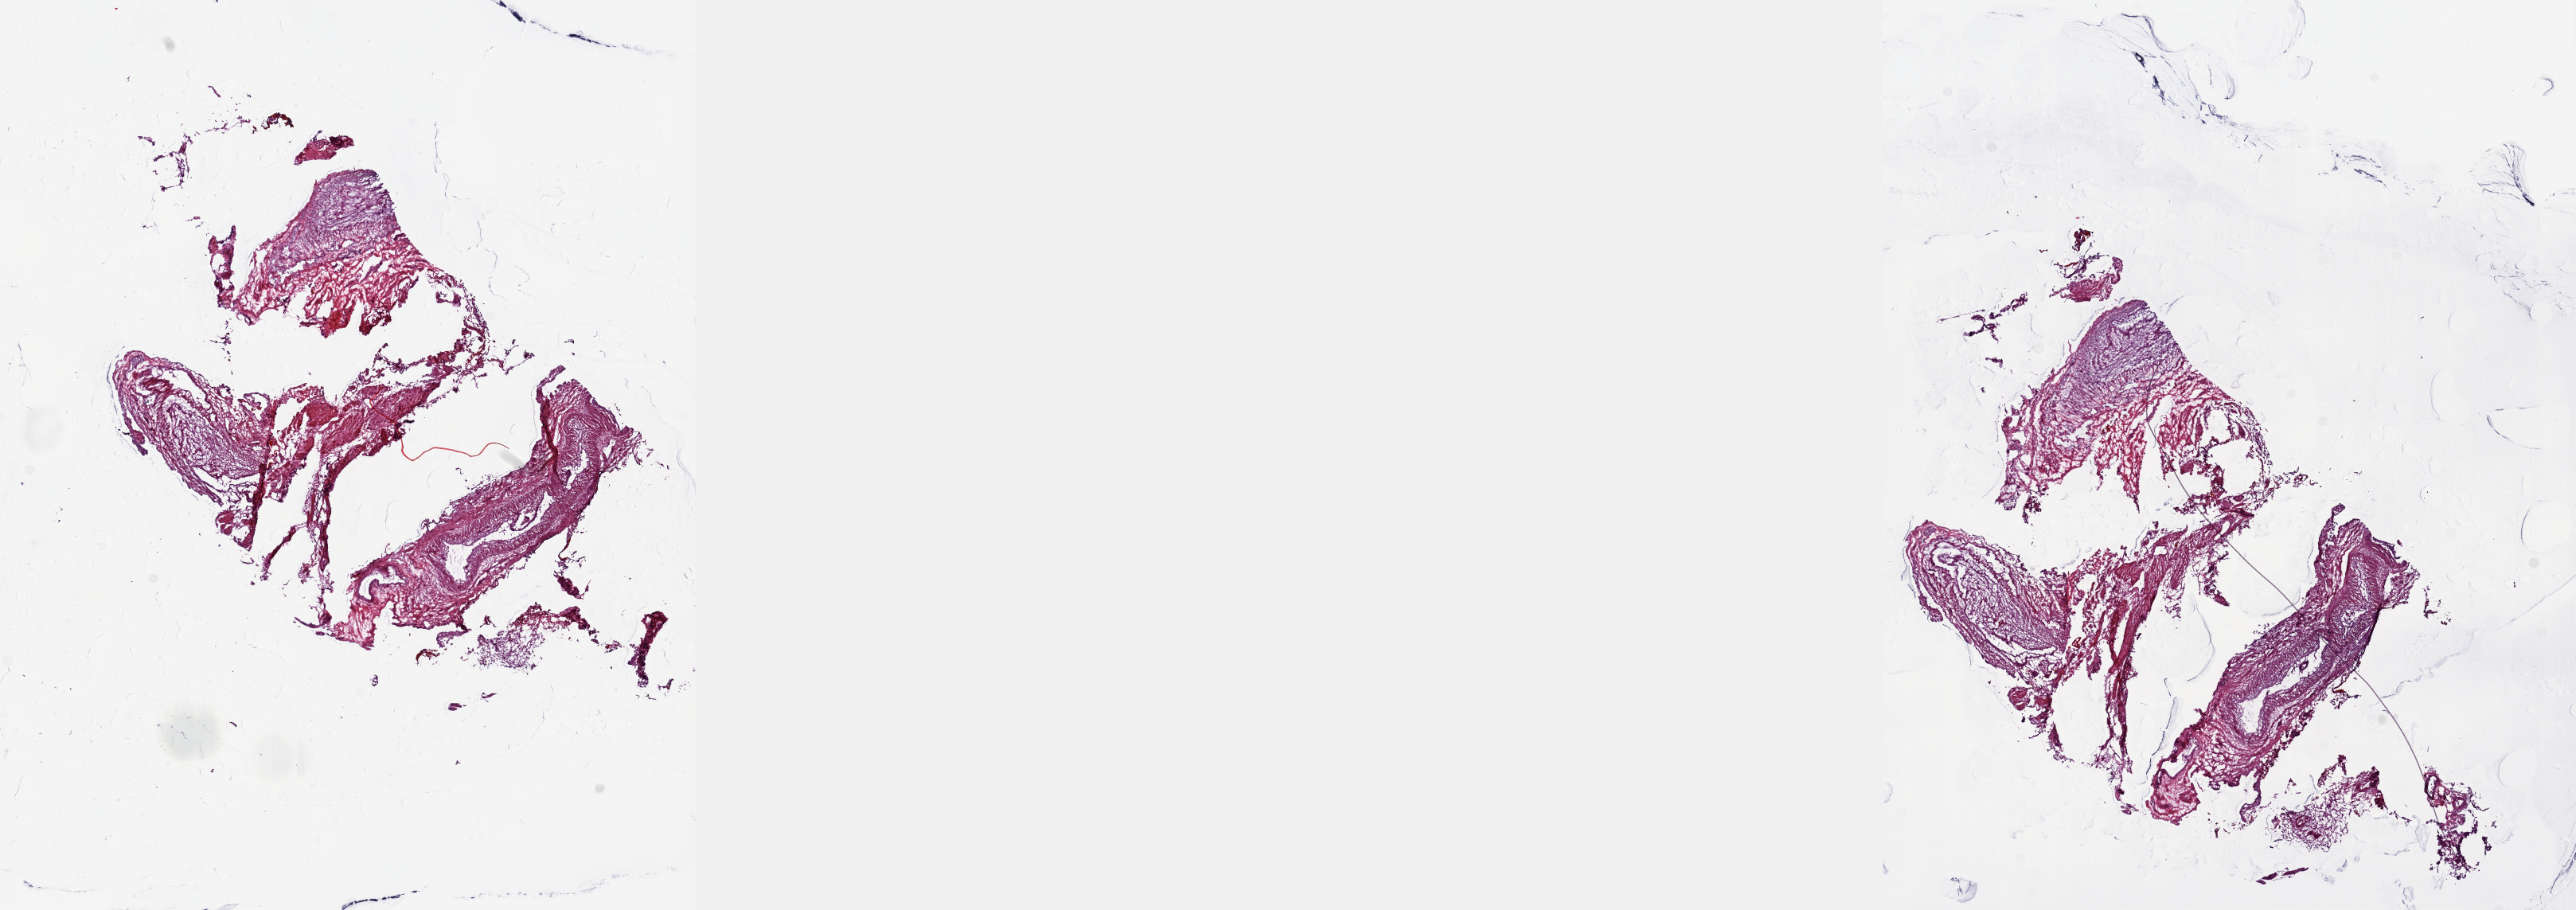
Digitized Hematoxylin and eosin (H&E) stained tissue section (whole slide) — a low-resolution overview of the entire scanned area, about 26.1 x 9.2 mm (acquisition: 20x scan), frozen section, prostate, solid tissue normal (non-tumour tissue) sample. Male, age 64 years at initial diagnosis. Composition of this section per pathologist review: tumour cells 0%, tumour nuclei 0%.
This section: solid tissue normal (non-tumour) sample from the same patient. Patient diagnosis: Adenocarcinoma, NOS (prostate gland).